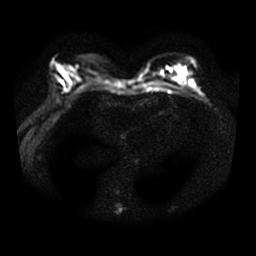
Breast MRI, one axial slice. Position 16 of 34 along the scan axis. Diffusion-weighted series; image 2 of 4 stored at this slice position (different b-values; order by instance number). 3 T. 256 × 256 image matrix, field of view 340 × 340 mm. Female patient.
Structures marked on this image (outlined manually by an expert reader):
- tumour on diffusion-weighted imaging: bounding box <176,65,185,75> (left, top, right, bottom; pixels)